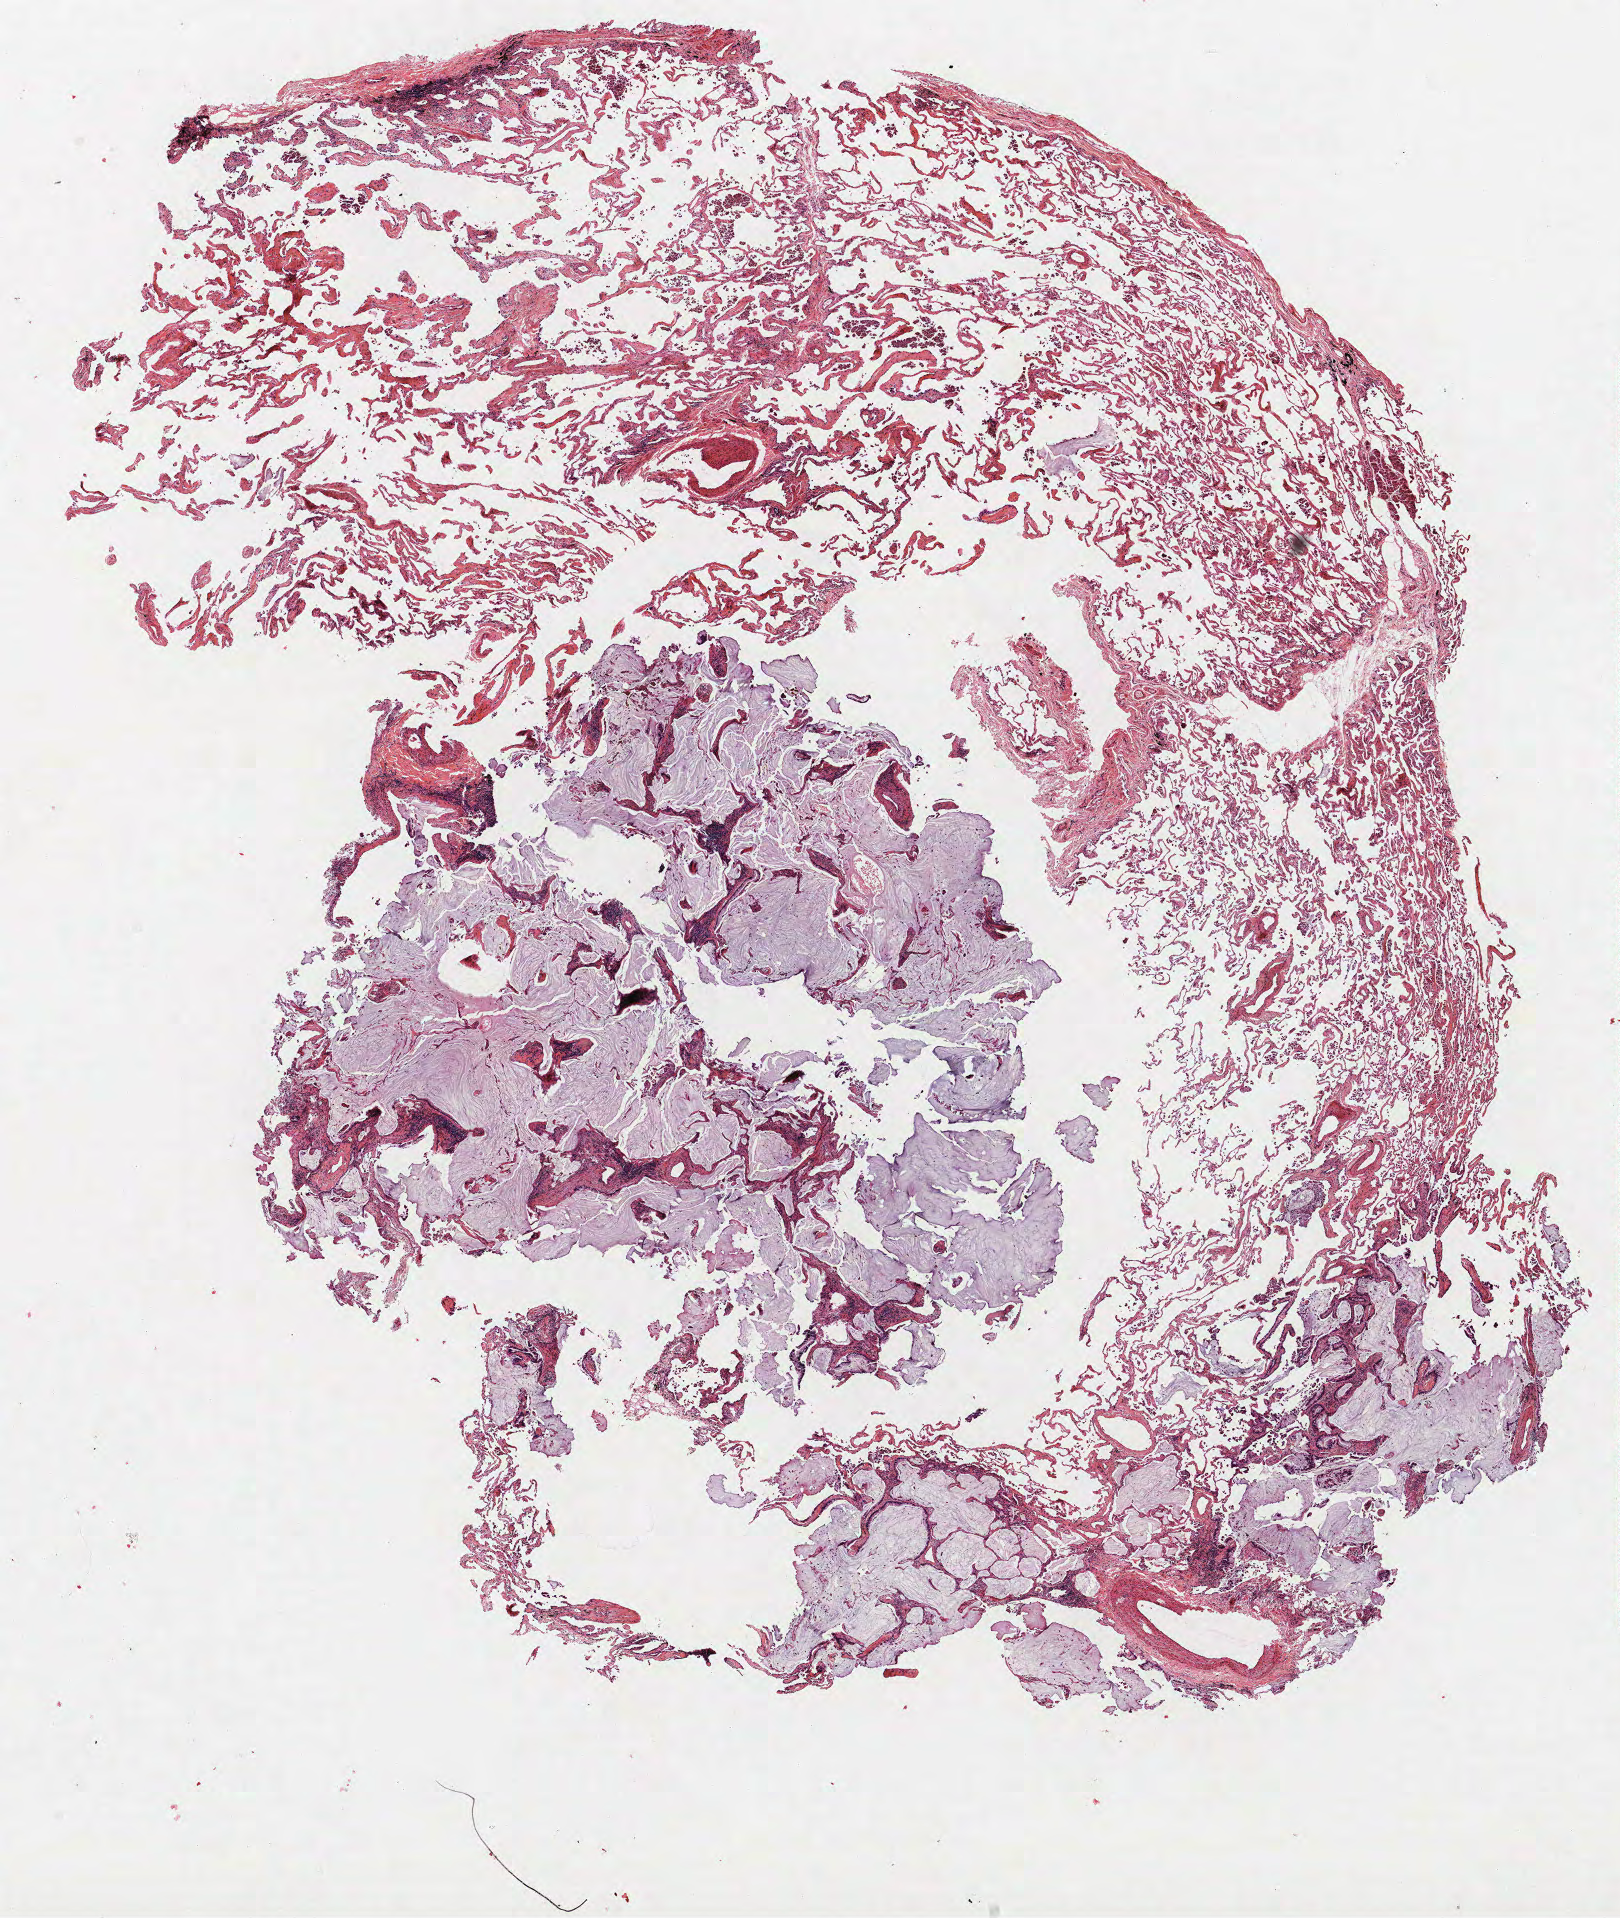
Hematoxylin and eosin (H&E) stained whole-slide image — a low-resolution overview of the entire scanned area, about 13.0 x 15.3 mm, formalin-fixed paraffin-embedded (FFPE) section, lung tissue. Male, age 66 at enrolment. Grade: well differentiated (G1).
Tumour size (pathology): 18 mm. ICD-O-3 topography: upper lobe of lung (C34.1). Primary tumour location (clinical record): left upper lobe. Participant's lung-cancer diagnosis: Bronchiolo-alveolar carcinoma, mucinous. Stage (AJCC 6th edition): IA.